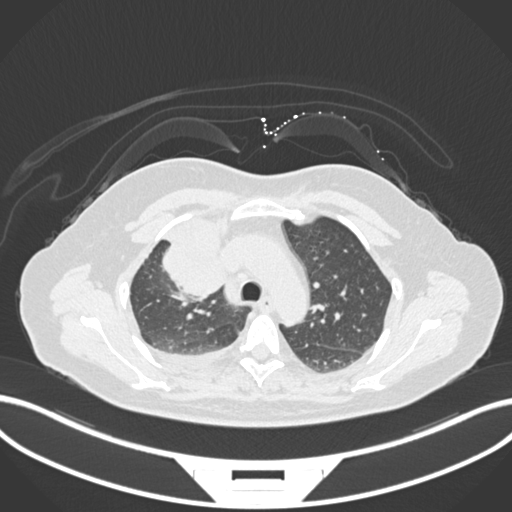
Chest CT, one axial slice. Slice 115 of 172 in the series (ordered by position). Reconstruction kernel B30f. 120 kVp. Lung window (W 1500 / L -600 HU). 1 mm slice thickness. 512 × 512 image matrix, field of view 400 × 400 mm. Female patient, age 52 years. From the clinical record (not read from this slice): clinical TNM (as recorded): T3 N1 M1.
Outlined on this slice (rectangle marked by the reading radiologist):
- lung tumour (recorded histology: adenocarcinoma): bounding box [x1, y1, x2, y2] px = [155, 207, 233, 301]